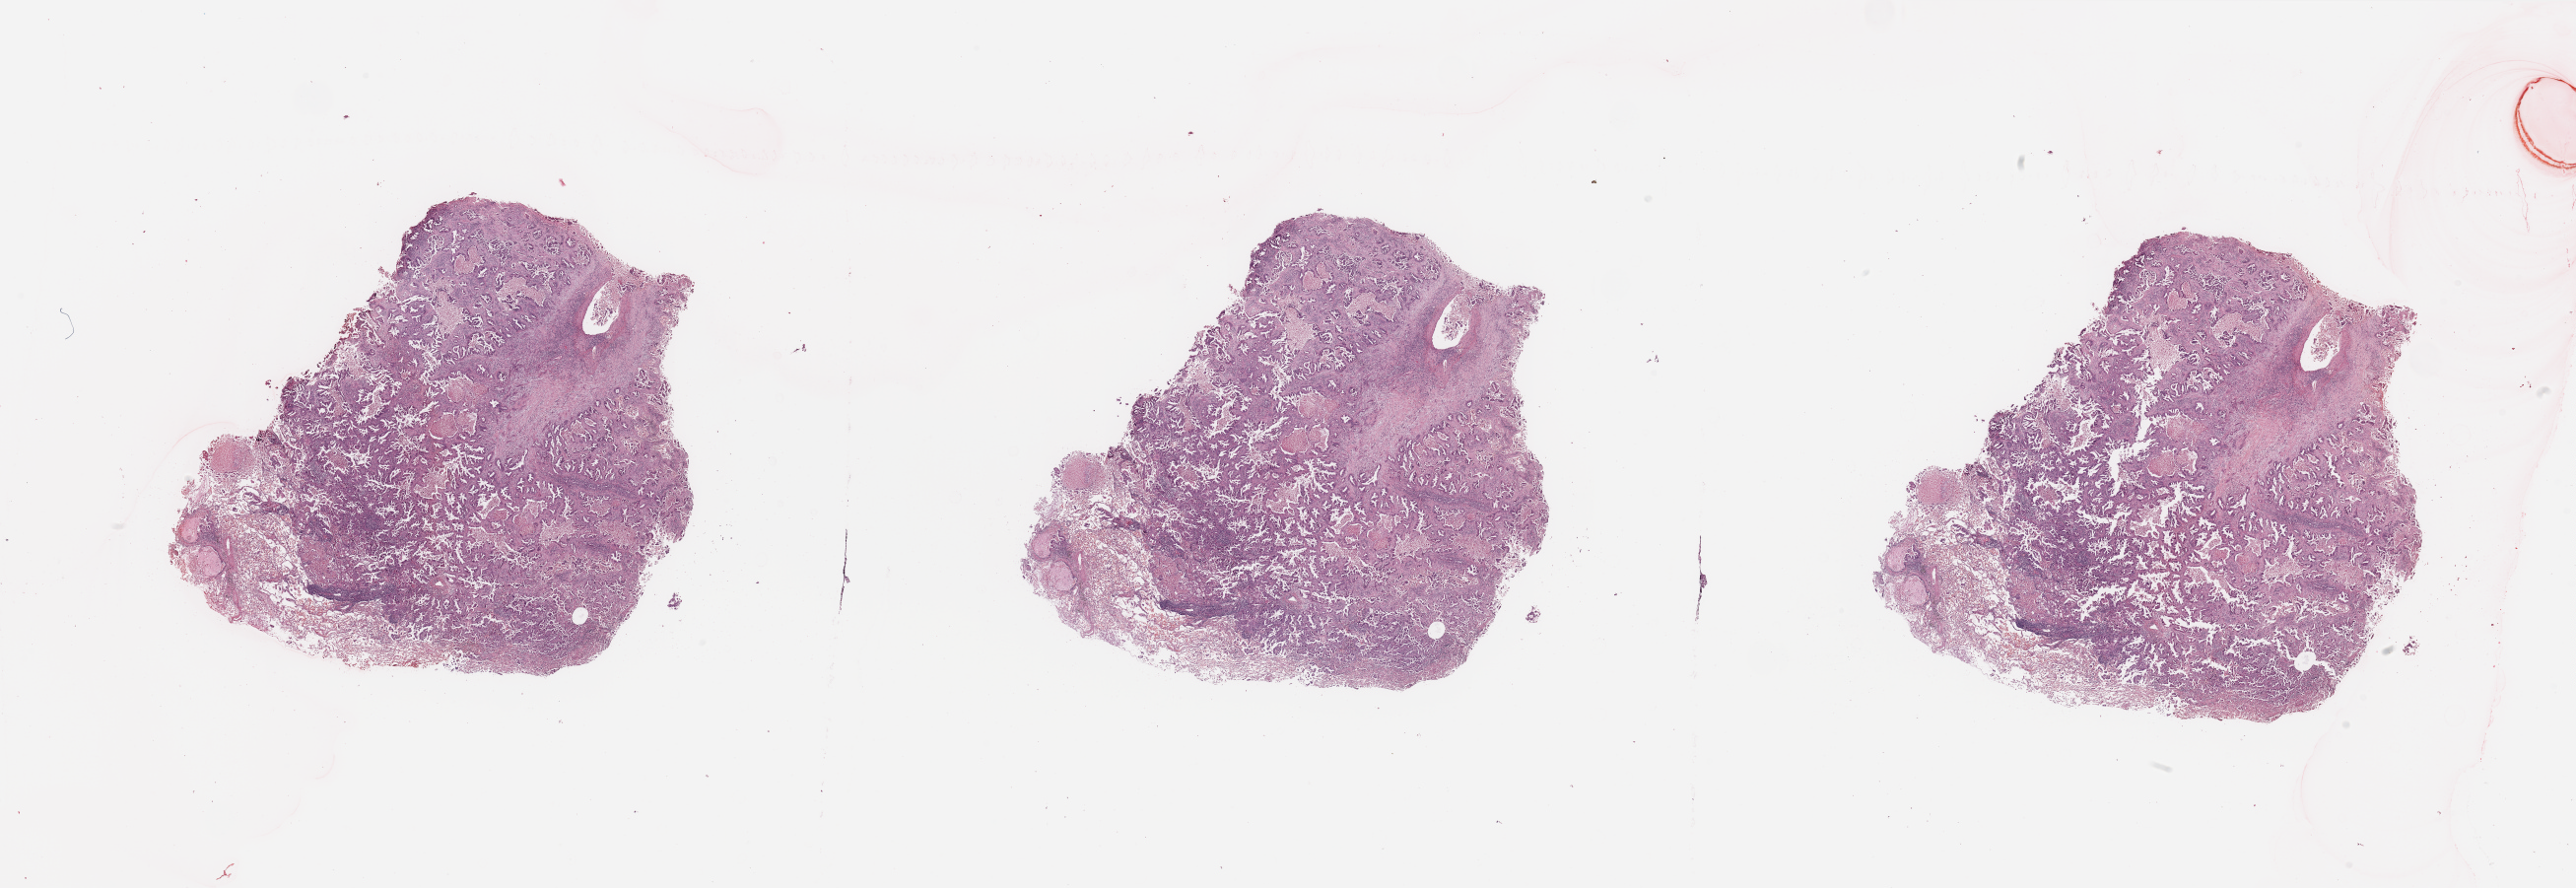
H&E whole-slide image, shown as a low-resolution overview of the whole scanned area (about 41.3 x 14.3 mm); lung, tumour tissue. Patient: female, age 73 years. Histologic grade: G2 (moderately differentiated).
AJCC pathologic stage: IIIA. Histologic diagnosis: Adenocarcinoma, NOS.